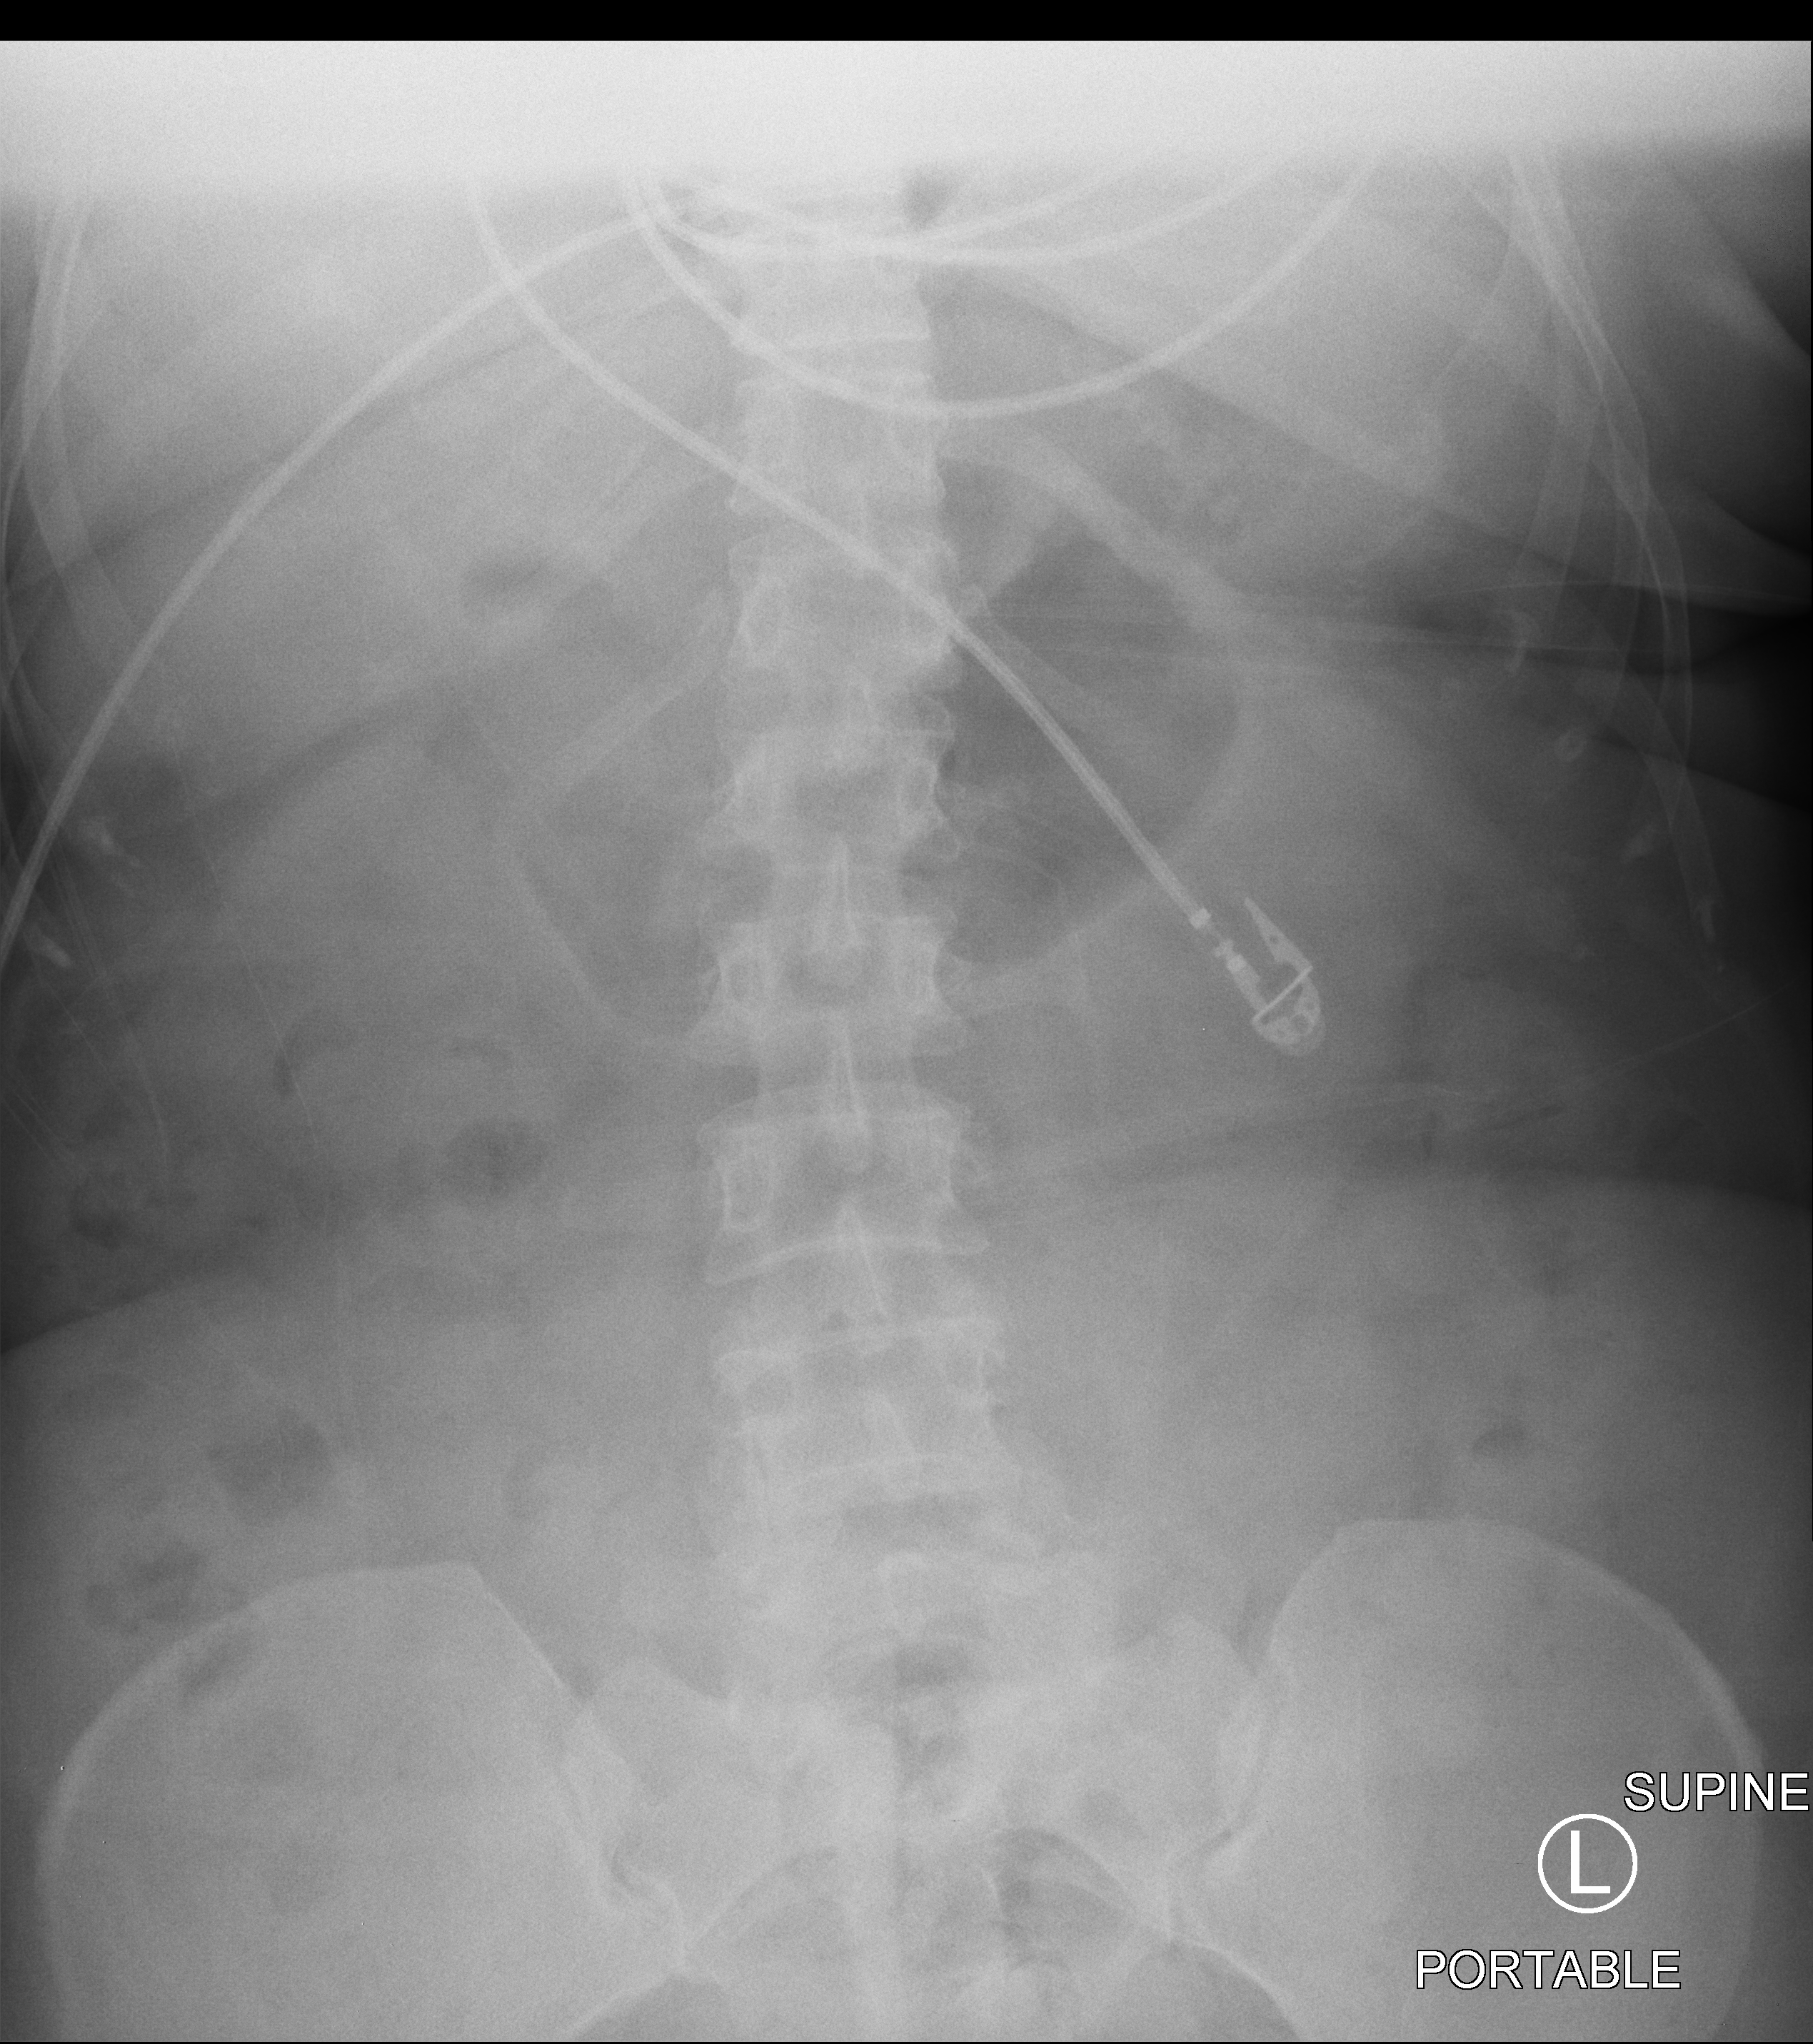
Abdomen X-ray (portable), anteroposterior (AP) projection. Female patient hospitalised with COVID-19, age 60–74 years.
From the hospital-stay record, not from the radiograph (when in the stay this image was taken is not recorded):
- mechanically ventilated during this hospital stay: yes
- admitted to intensive care during this hospital stay: yes